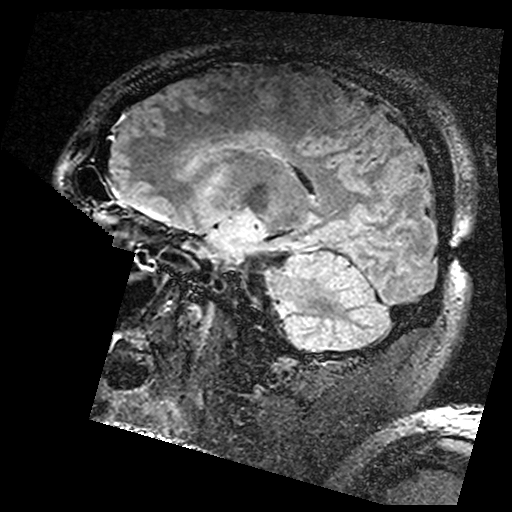
Brain MRI from a brain-tumour surgery series, one sagittal slice; position 106 of 176 along the scan axis; T2 FLAIR; 1 mm slice thickness; 512 × 512 image matrix. From the clinical record (not read from this slice): histopathology: Astrocytoma; WHO grade: 3.
Structures marked on this image (expert manual segmentation):
- residual tumour: bounding box <208,175,224,189> (left, top, right, bottom; pixels)